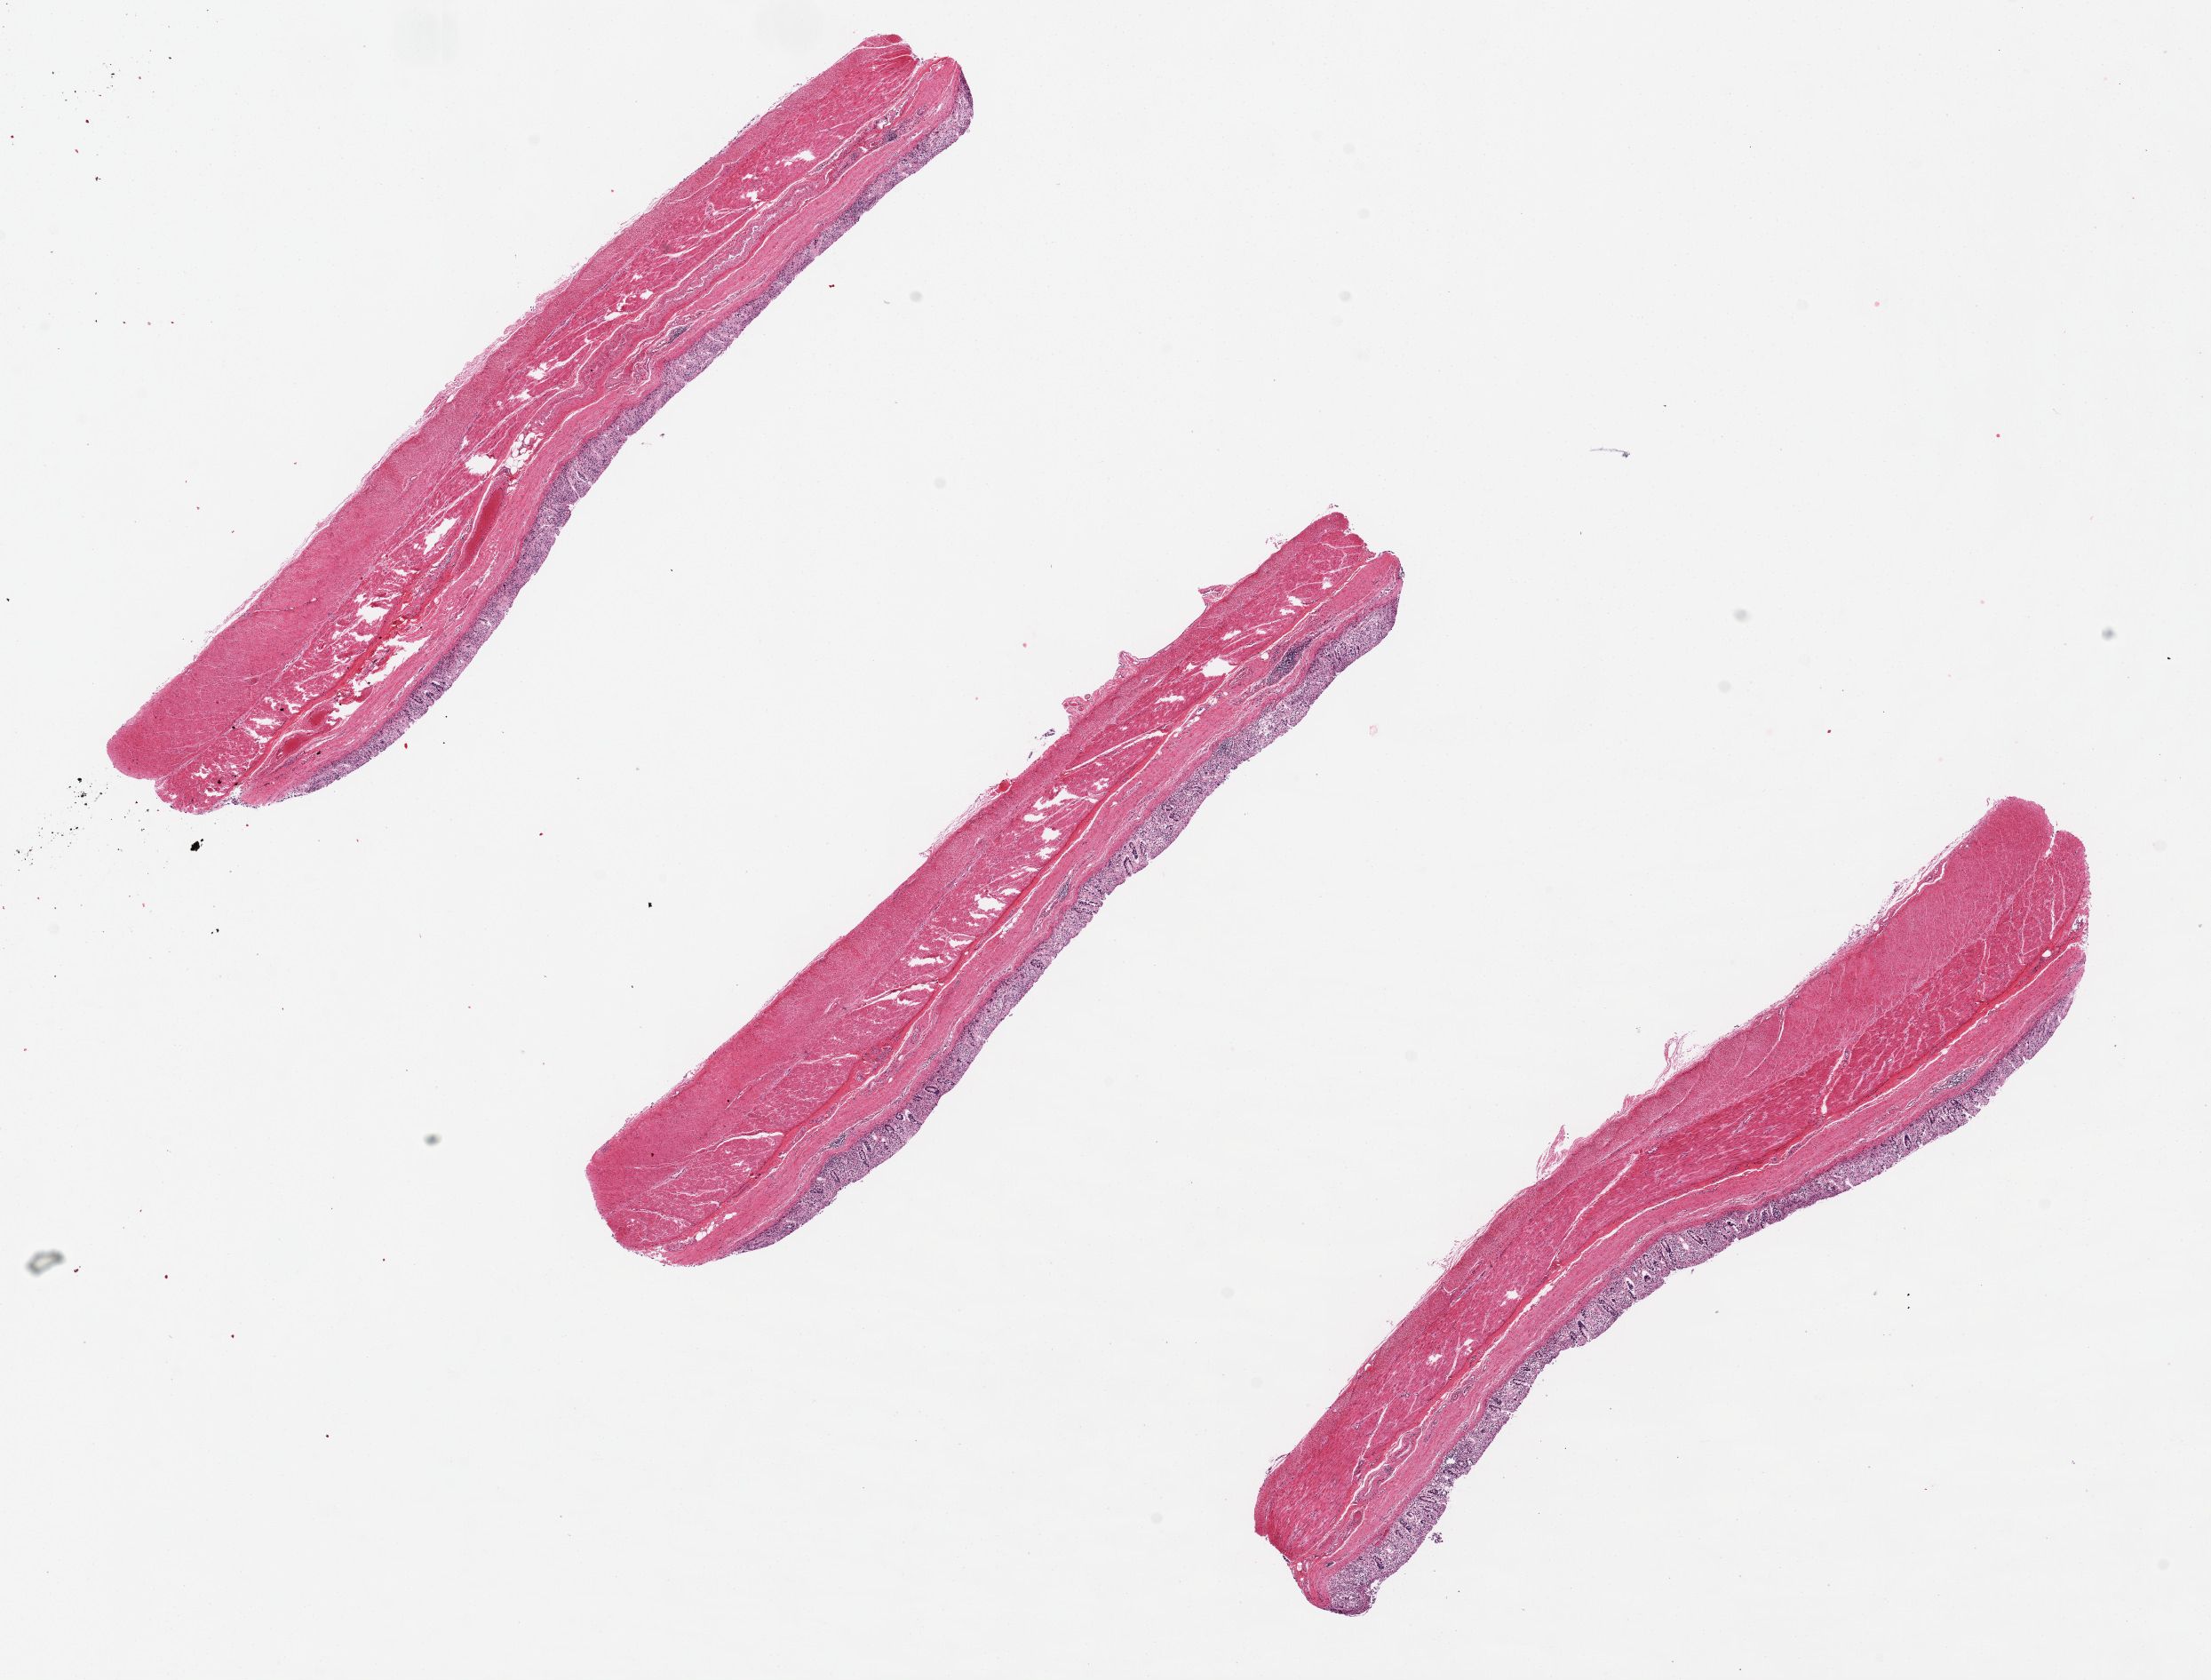
Haematoxylin and eosin whole-slide image, shown as a low-resolution overview of the whole scanned area (about 19.7 x 15.0 mm, slide scanned at 20x); PAXgene-fixed, paraffin-embedded tissue; section of transverse colon (target tissue); donor tissue sample. Donor sex: female.
• review note (as recorded): Mucosa, 1 wall. Three pieces: